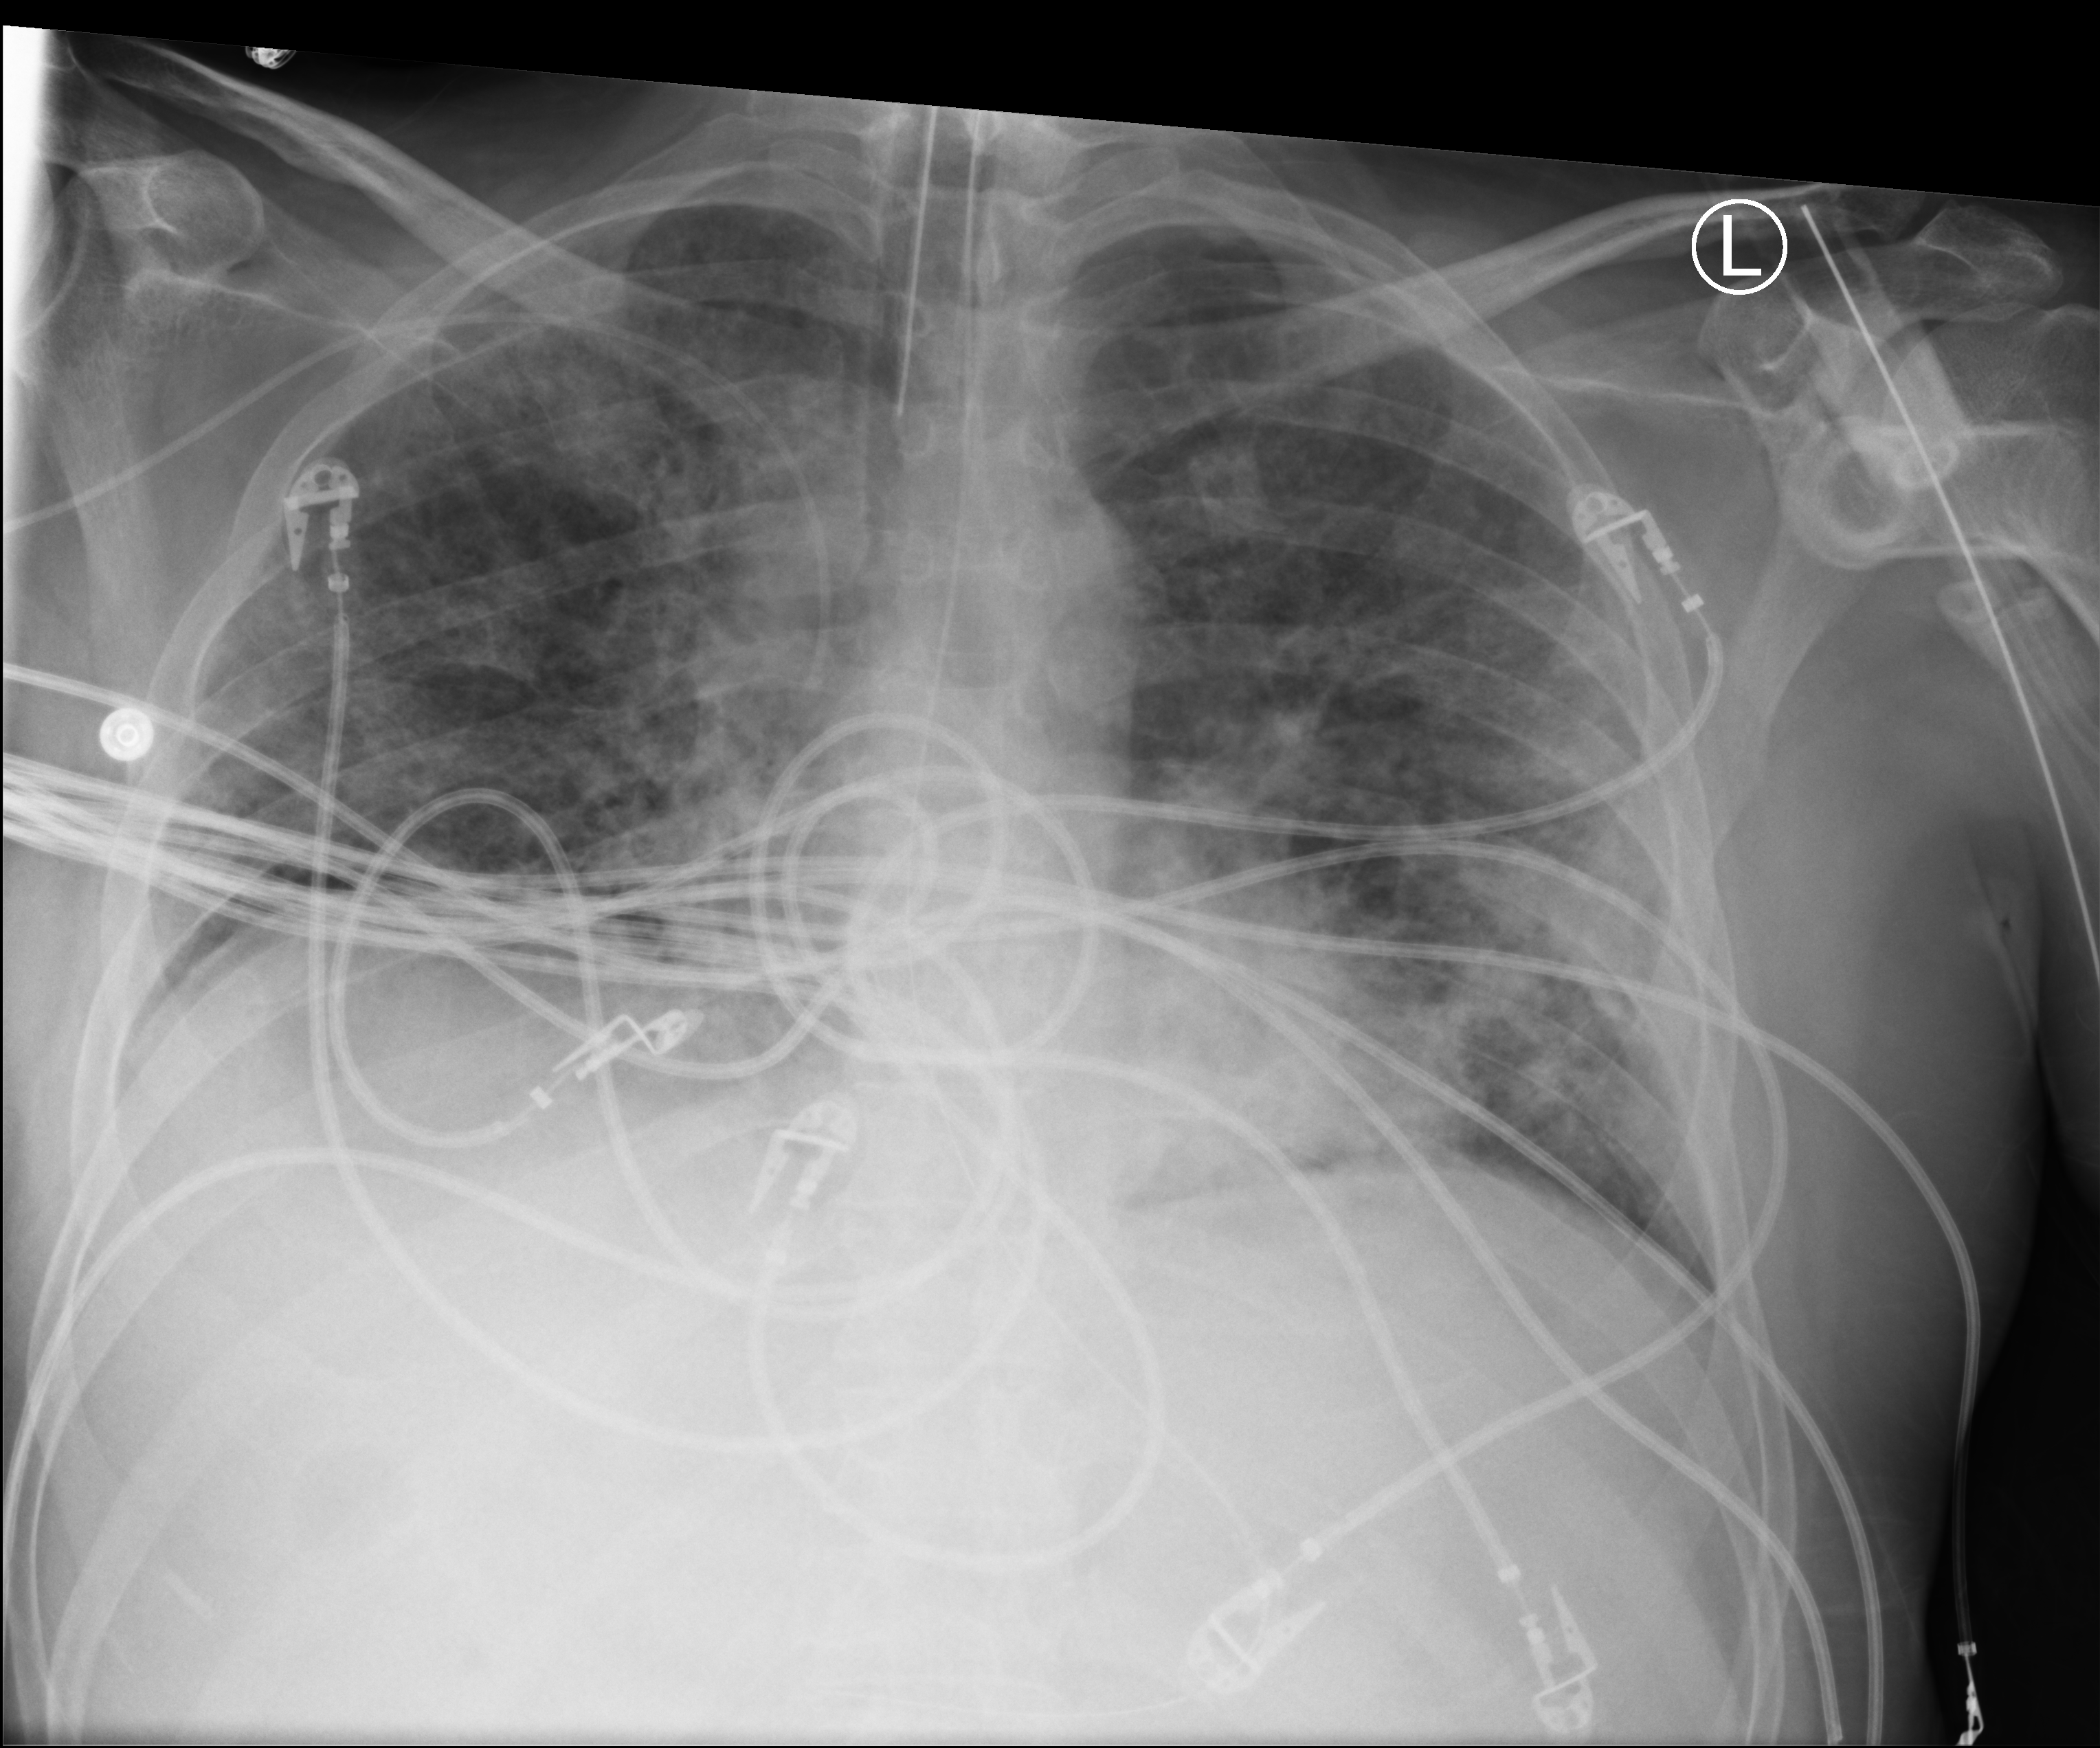
Portable chest radiograph, anteroposterior (AP) projection. Patient hospitalised with COVID-19; male, aged 18–59 years.
Hospital-stay facts (about this admission, not read from this image; timing relative to this image not recorded): admitted to intensive care during this hospital stay: yes.